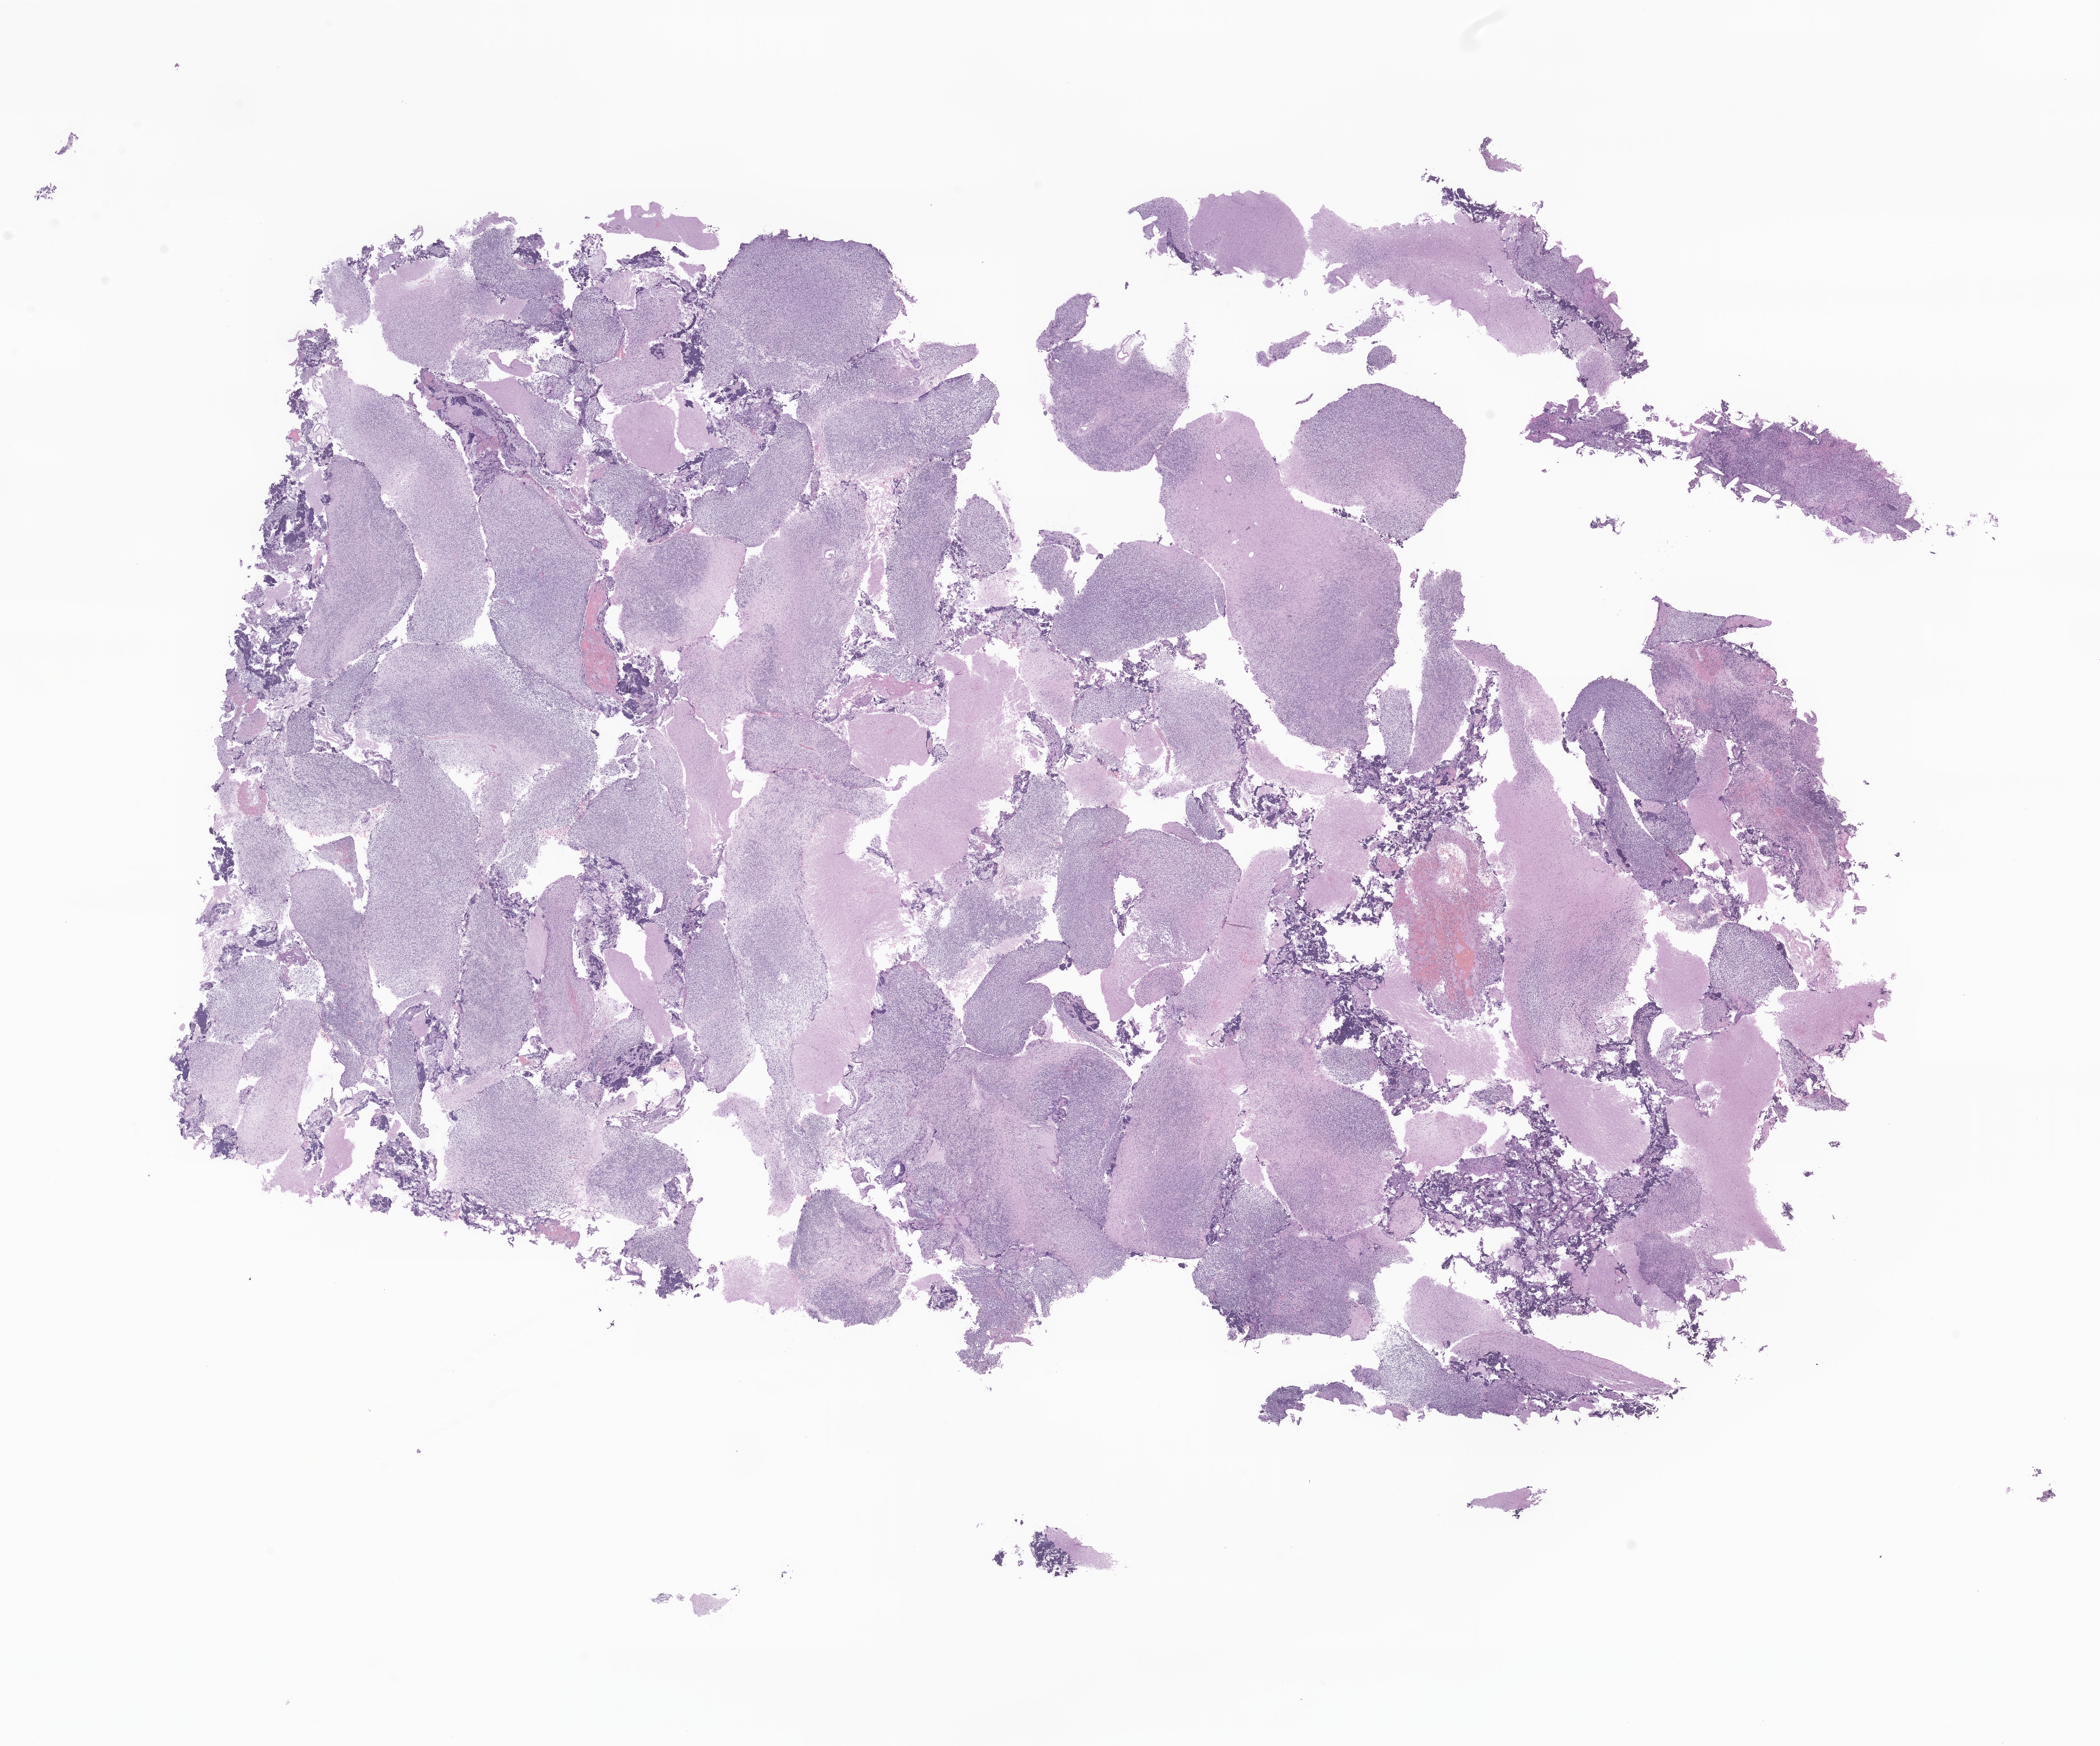
Digitized haematoxylin and eosin-stained section of tumor tissue from the cerebellum, low-resolution overview of the scanned area, about 23.0 x 19.1 mm; formalin-fixed paraffin-embedded section. Male patient, age 69 months (5 years 9 months).
Diagnosis: Tumor cells, malignant.